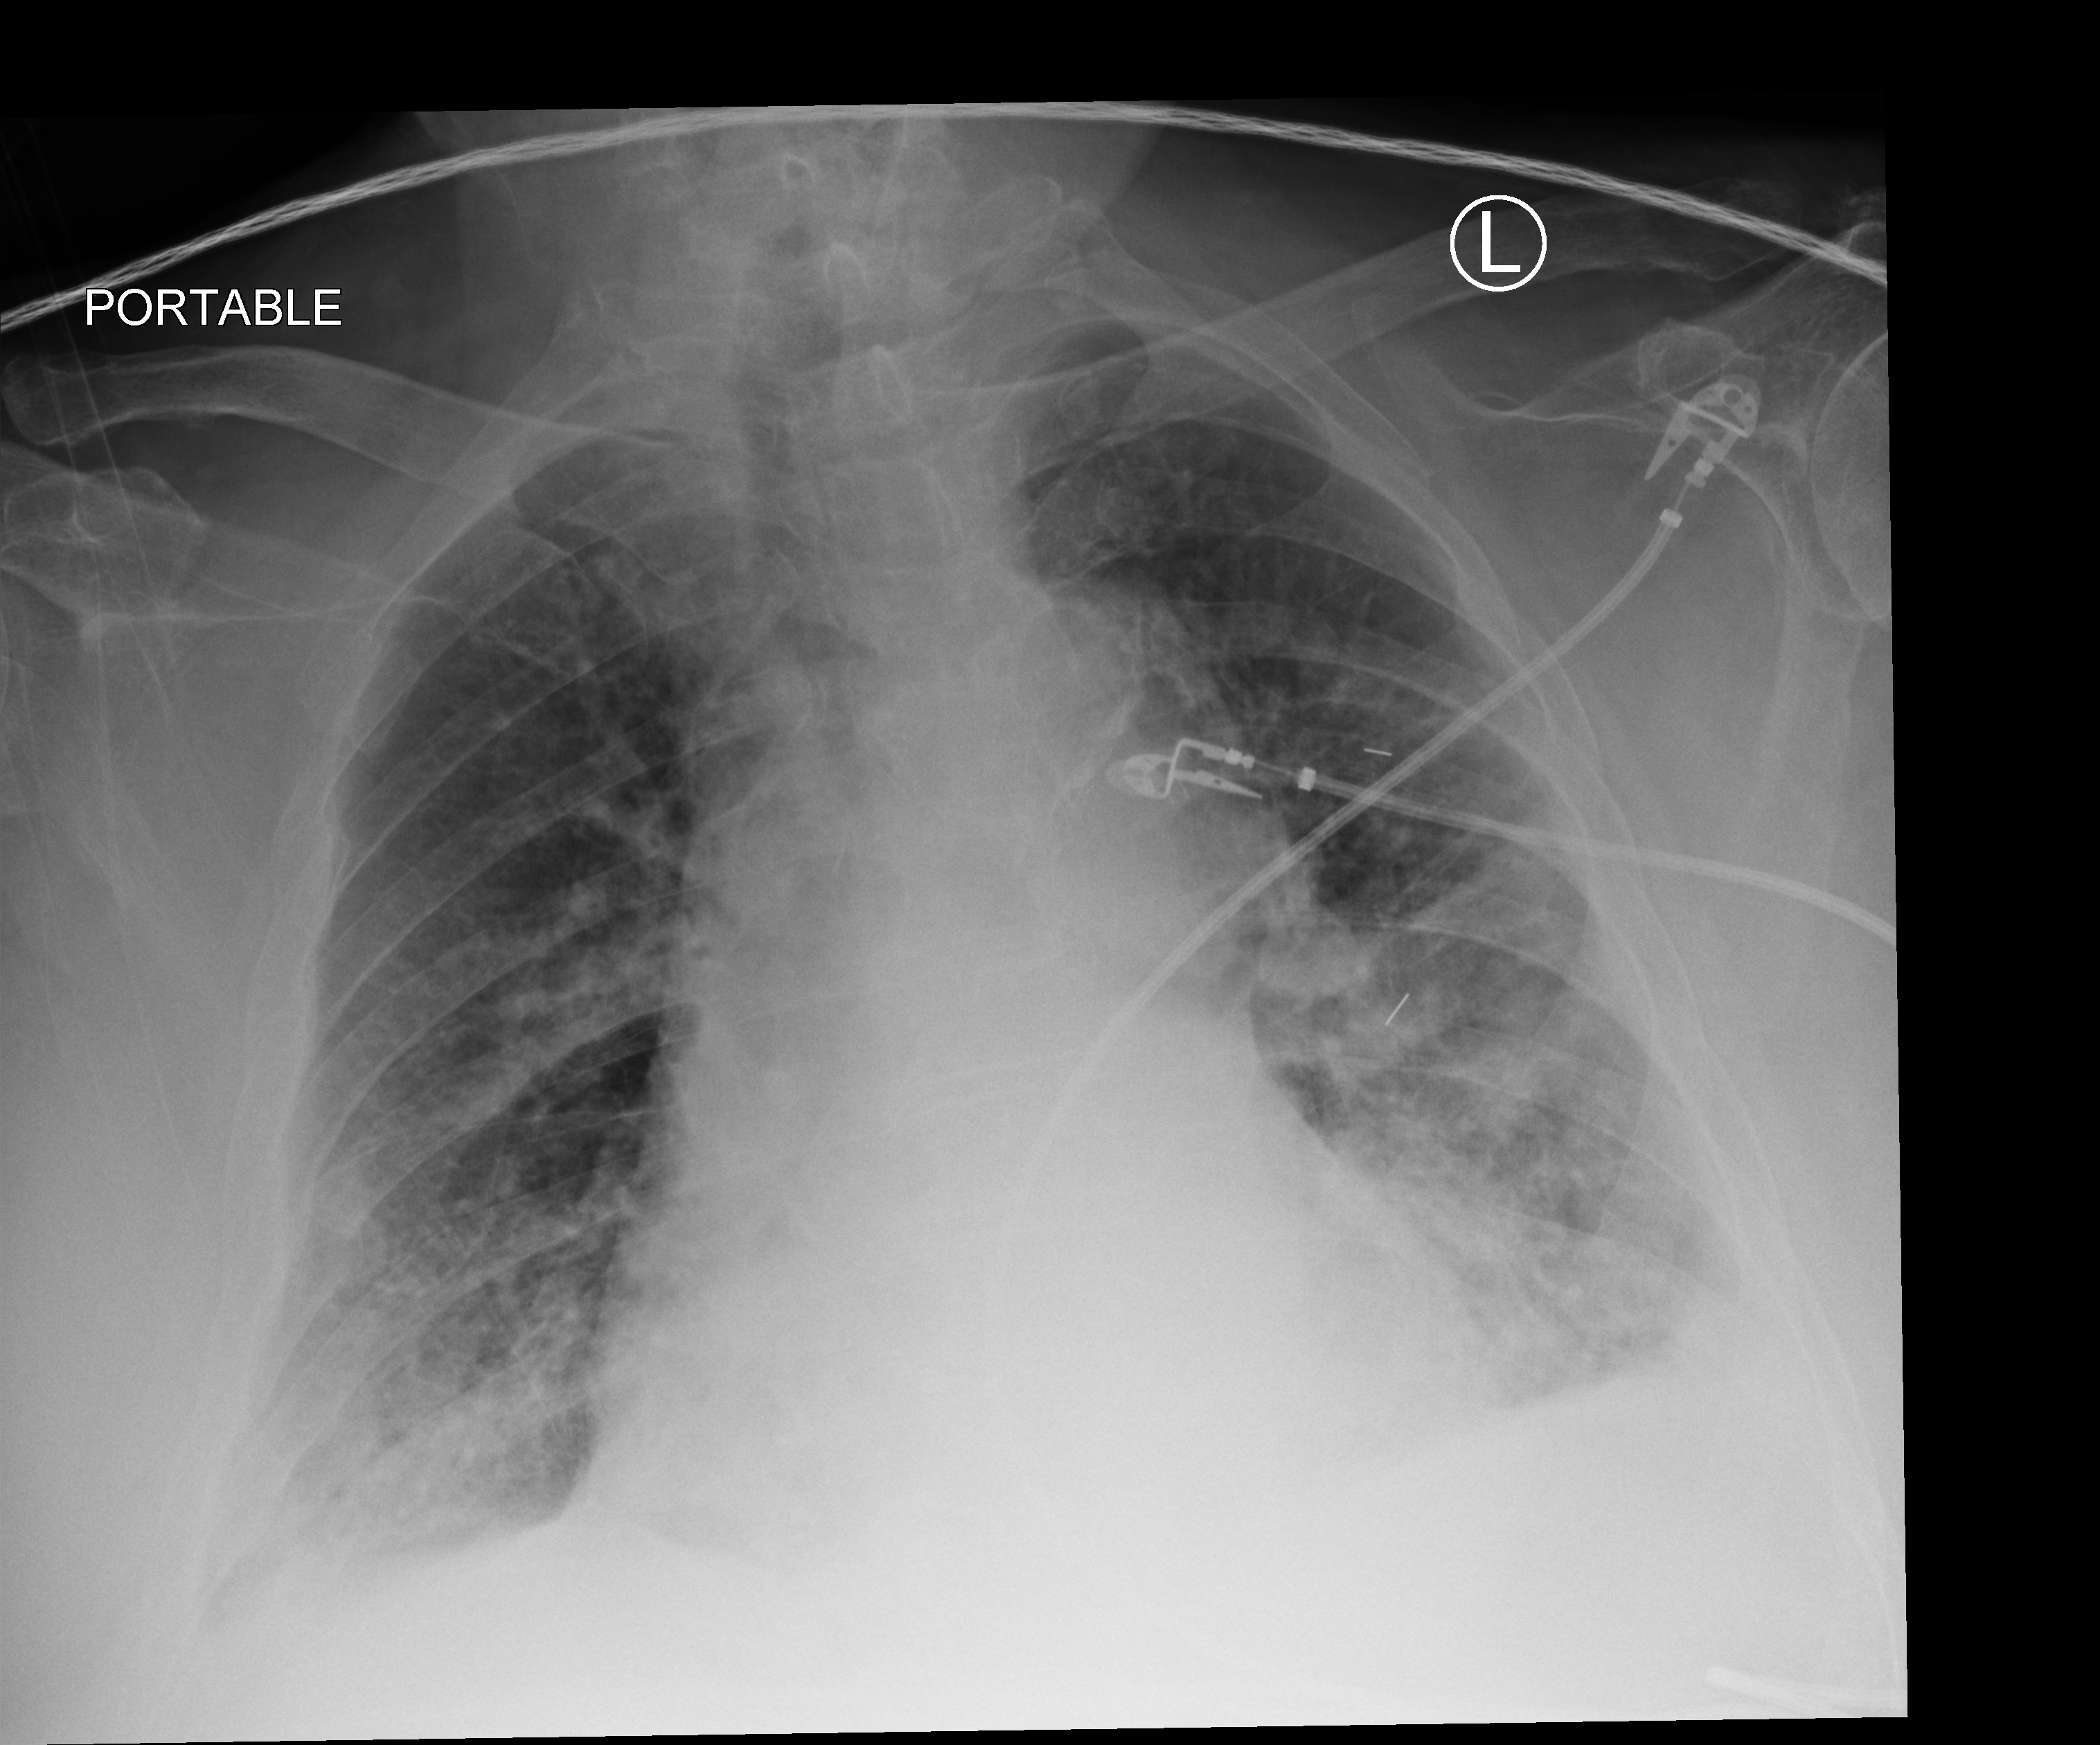
Portable chest radiograph, anteroposterior (AP) projection. Patient hospitalised with COVID-19; male, aged 75–90 years.
From the hospital-stay record, not from the radiograph (when in the stay this image was taken is not recorded):
- COPD (admission record): yes